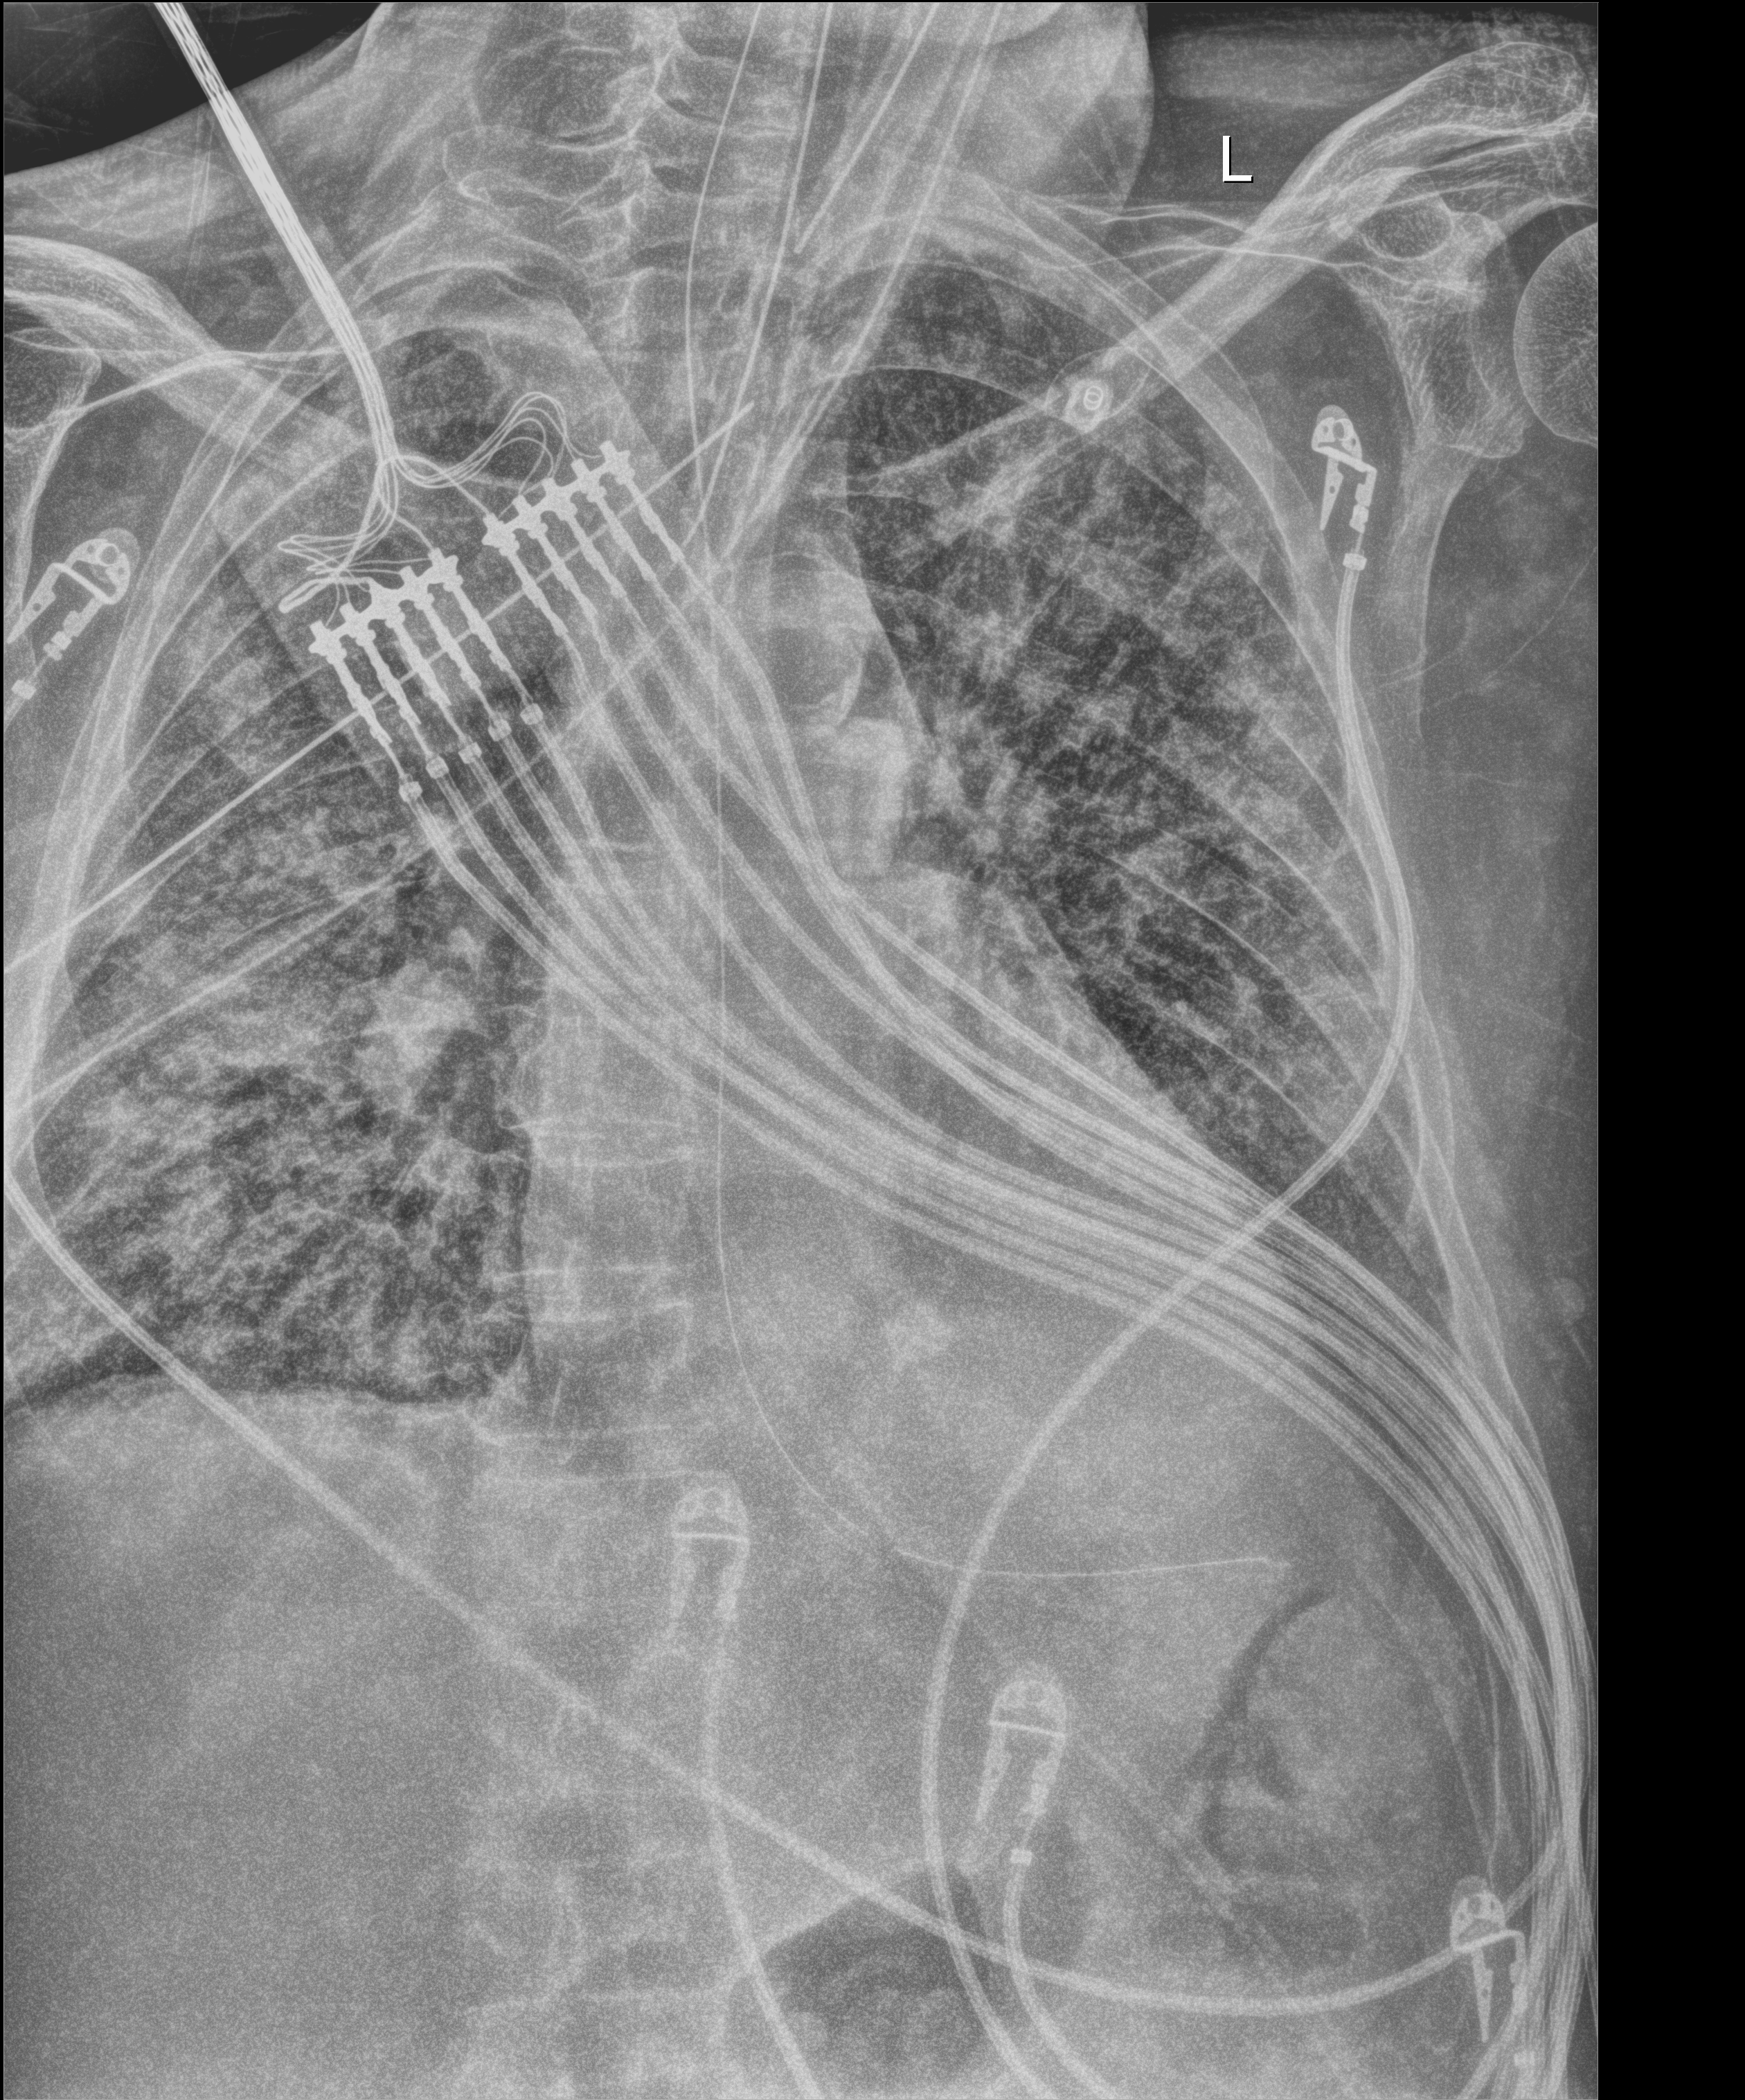
Portable chest radiograph, anteroposterior (AP) projection. Male patient hospitalised with COVID-19, age 60–74 years.
From the hospital-stay record, not from the radiograph (when in the stay this image was taken is not recorded): admitted to intensive care during this hospital stay: yes.